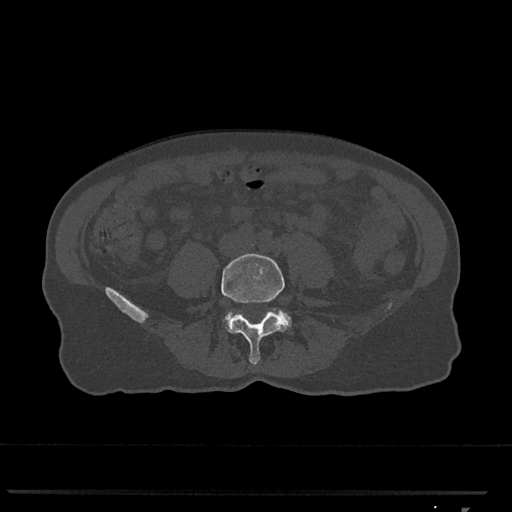
CT including the spine, one axial slice. Position 195 of 793 along the scan axis. Reconstruction kernel Br40s/3. 120 kVp. Bone window (W 1800 / L 400 HU). 0.5 mm slice thickness. 512 × 512 image matrix, field of view 380 × 380 mm. Female patient, age 62 years. Case-level facts recorded for this patient, not image findings: primary cancer: renal.
Annotated regions visible in this slice (semi-automatically segmented with operator editing):
- L4 vertebra: bounding box <221,253,287,365> (left, top, right, bottom; pixels)
- L5 vertebra: <225,310,291,328>